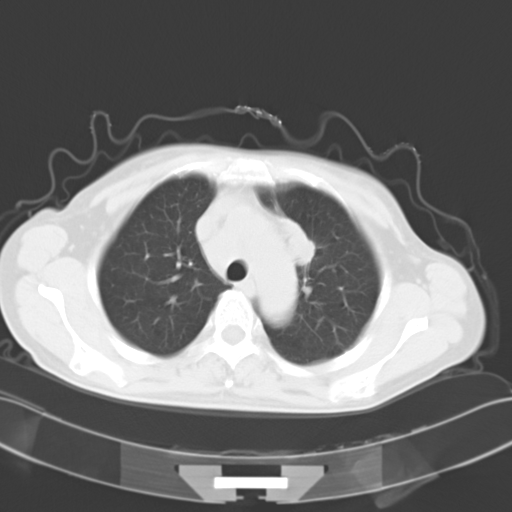
Chest CT, one axial slice. Position 21 of 27 along the scan axis. Reconstruction kernel B40f. Lung window (W 1500 / L -600 HU). 10 mm slice thickness. 512 × 512 image matrix. Female patient, age 50 years. Case-level facts recorded for this patient, not image findings: clinical TNM (as recorded): T2a N1 M1c.
Structures marked on this image (rectangle marked by the reading radiologist):
- lung tumour (recorded histology: adenocarcinoma): box from (x=278, y=214) to (x=312, y=268) px